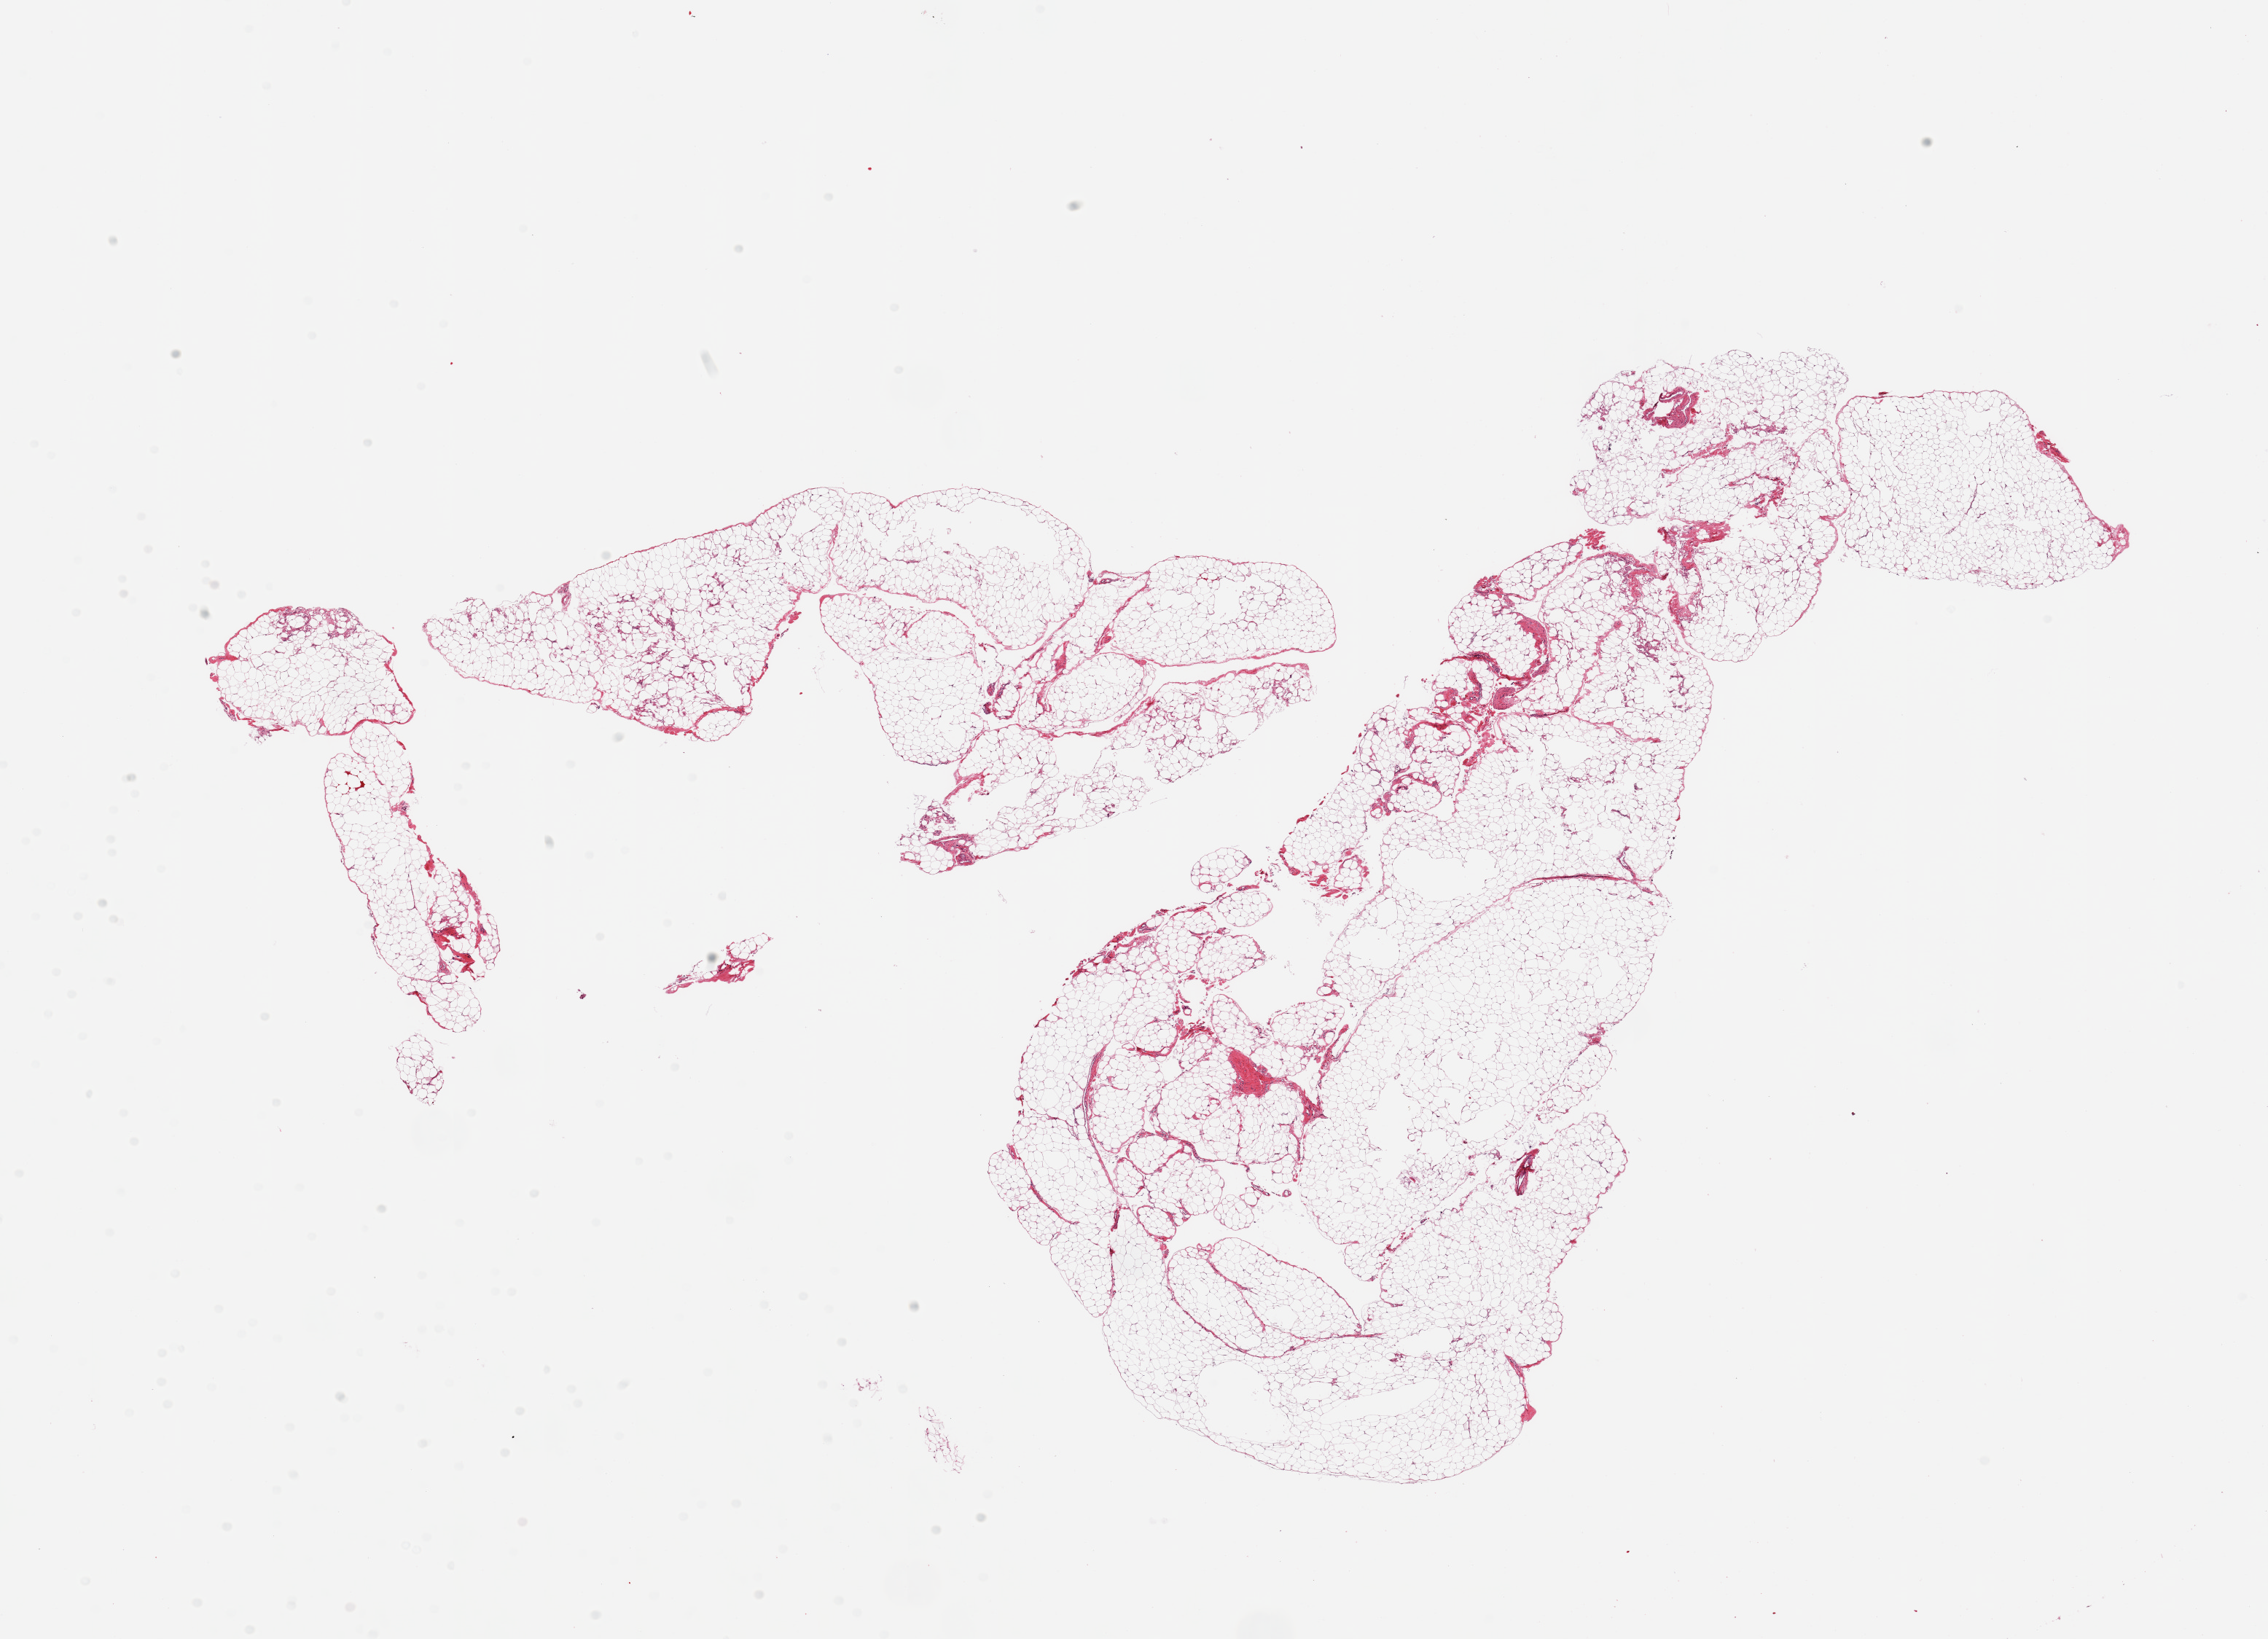
Hematoxylin and eosin (H&E) whole-slide image, a low-resolution overview of the entire scanned area, about 24.6 x 17.8 mm (slide scanned at 20x), PAXgene-fixed paraffin-embedded (PFPE) section, target tissue: omentum, donor tissue sample.
Review note (as recorded): 2 pieces, 5% fascia/vascular elements.